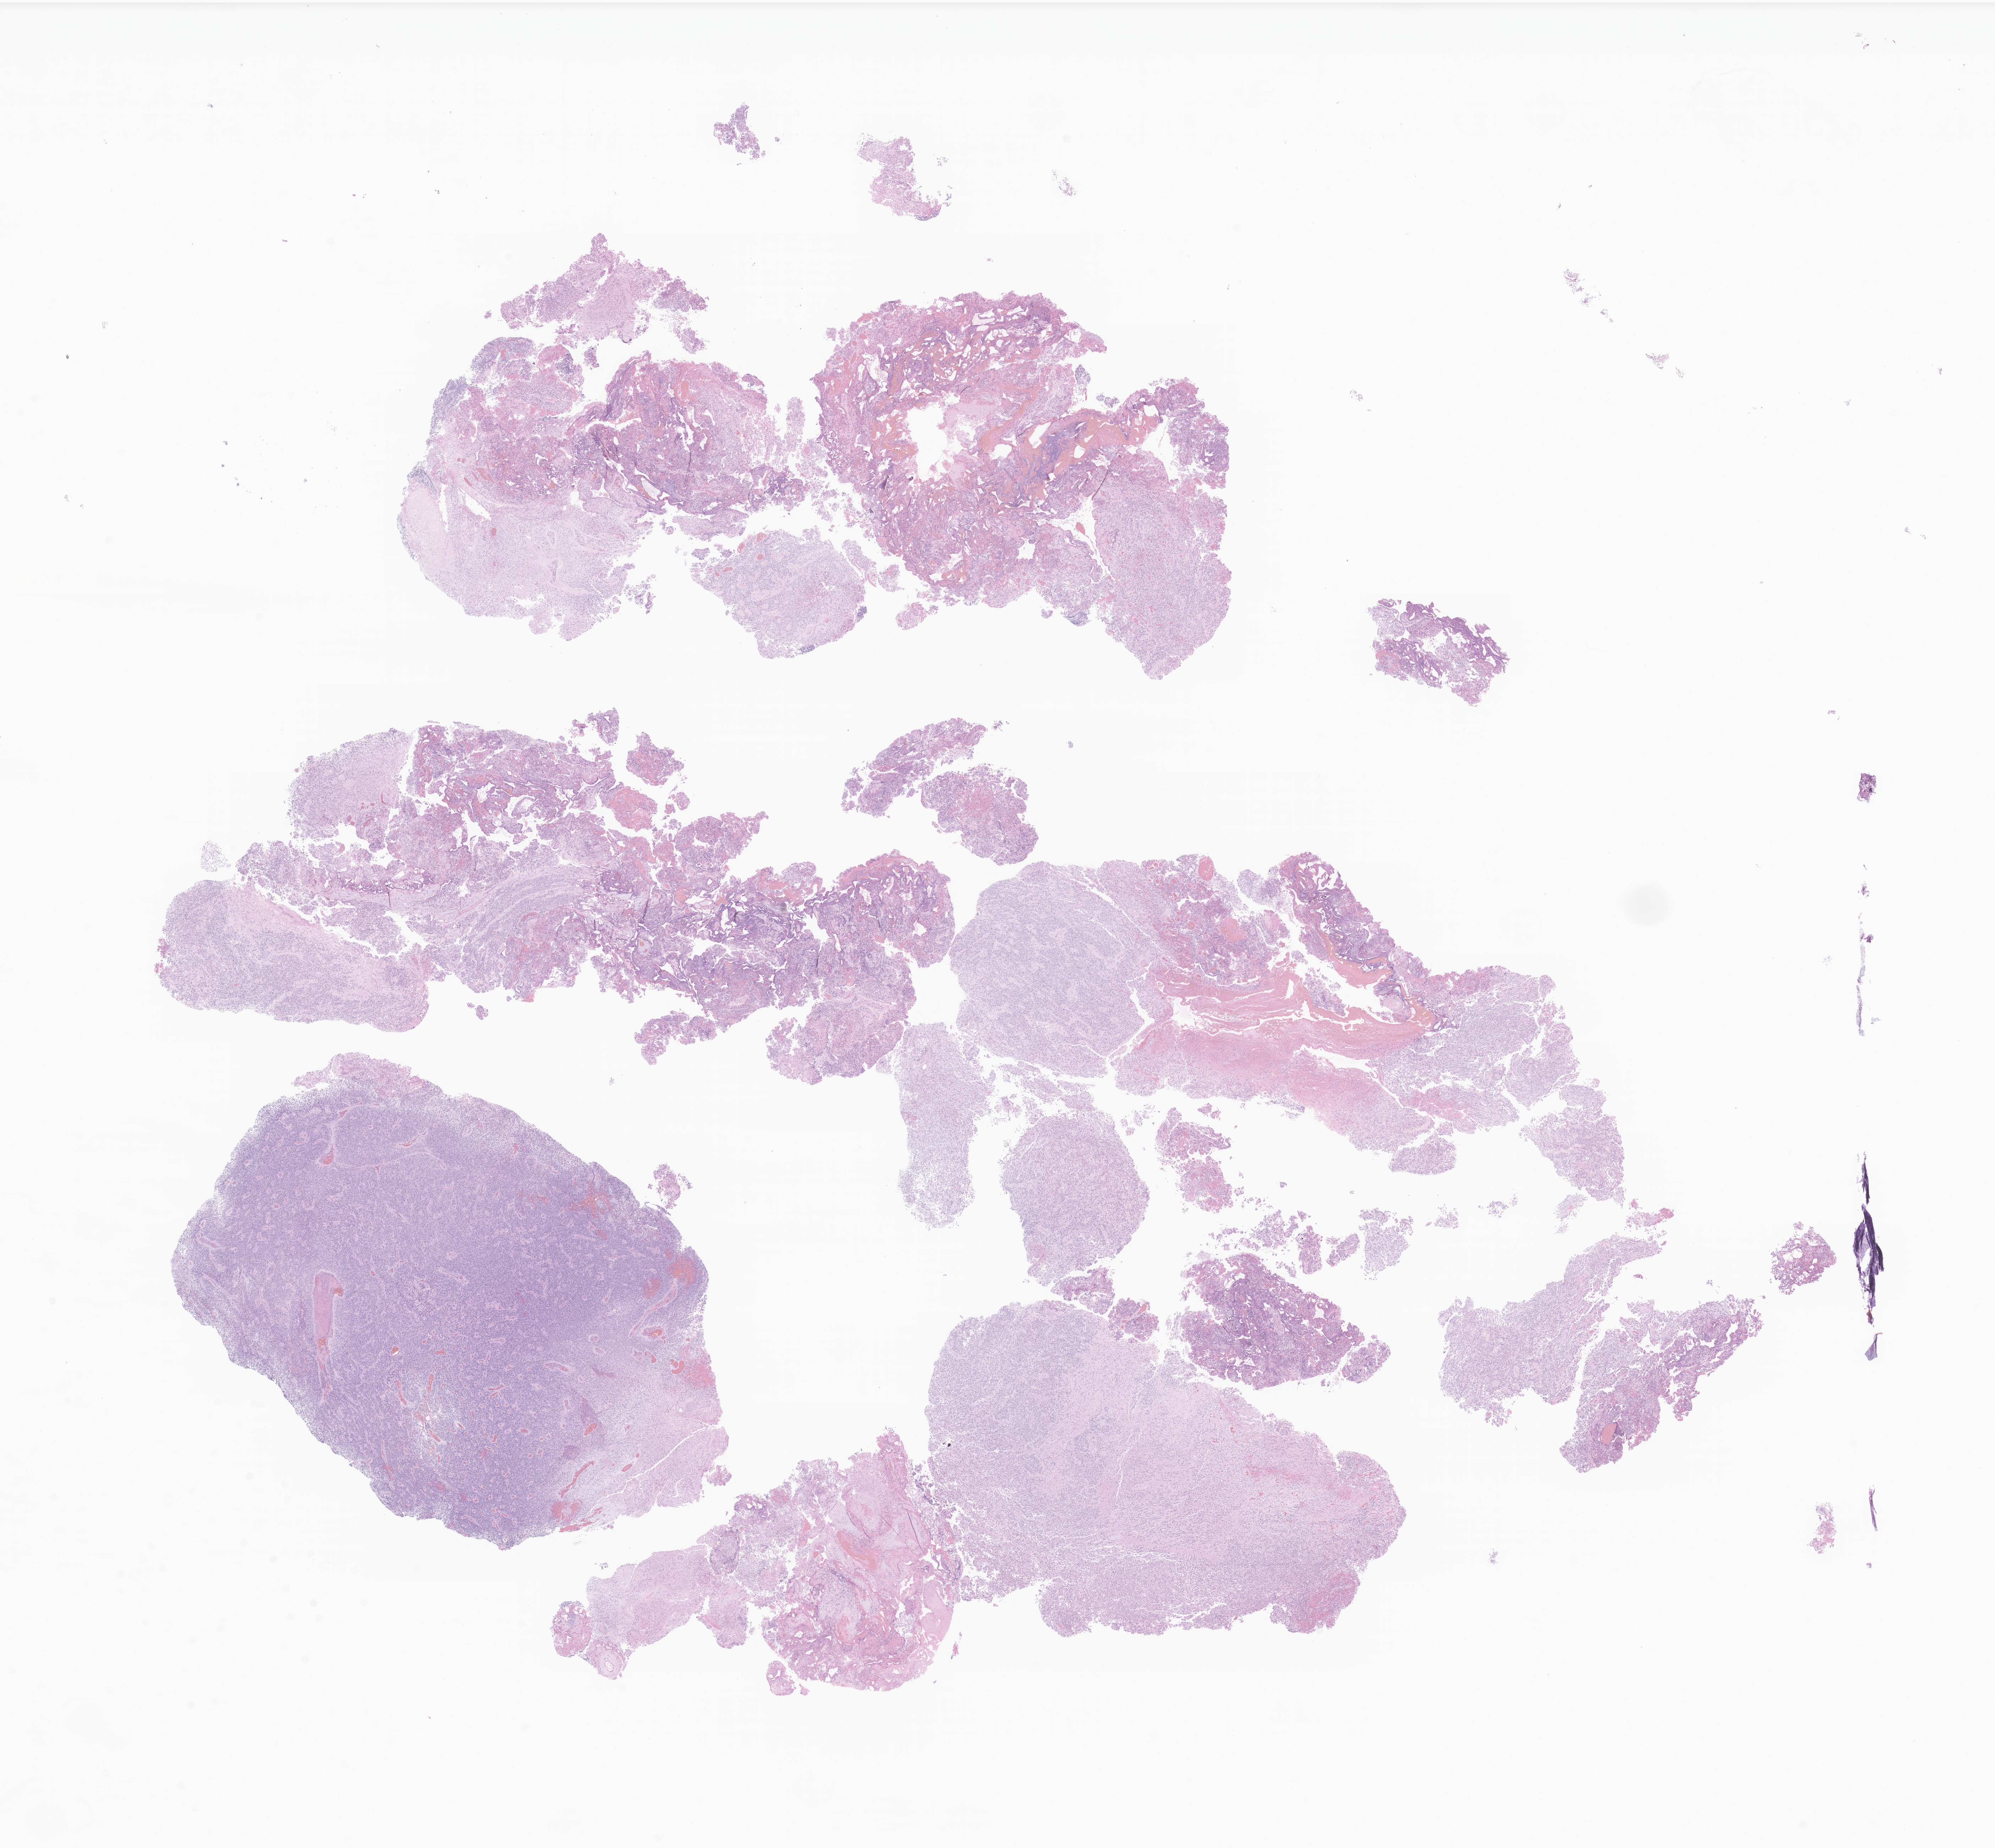
Digitized haematoxylin and eosin-stained section of tumor tissue from the cerebral ventricle, shown as a low-resolution overview of the whole scanned area (about 23.7 x 22.0 mm), formalin-fixed, paraffin-embedded (FFPE) tissue. Patient: male, age 52 months.
Diagnosis: Ependymoma, NOS.